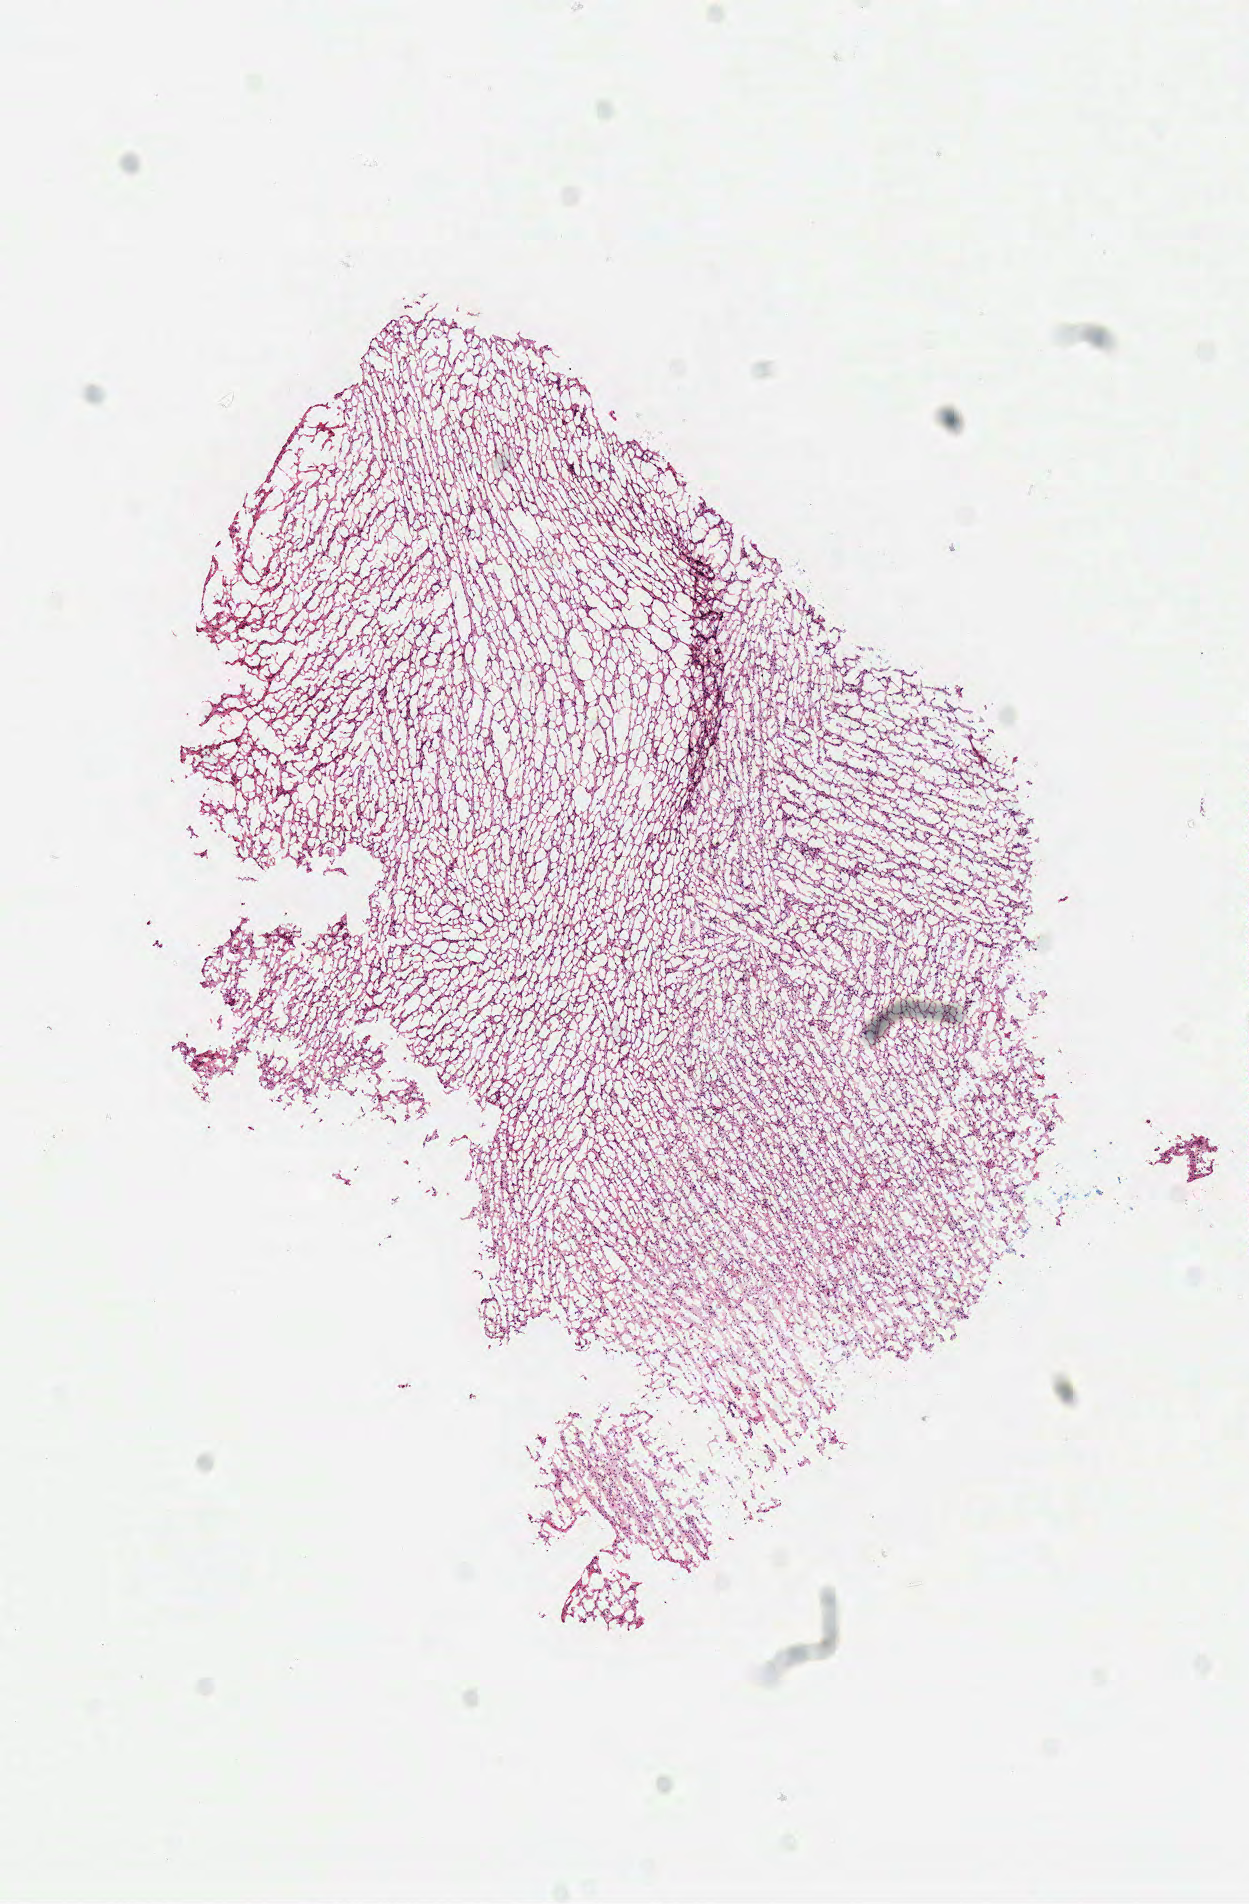
Digitized H&E-stained tissue section (whole slide) — shown as a low-resolution overview of the whole scanned area (about 4.9 x 7.5 mm, slide scanned at 40x). Frozen section from the top of the tissue portion. Brain, primary tumour sample. Female, age 52 years at initial diagnosis. Slide review estimates, as recorded: tumour cells 100%, tumour nuclei 70%, normal cells 0%, stromal cells 0%, necrosis 0%.
Diagnosis: Glioblastoma.